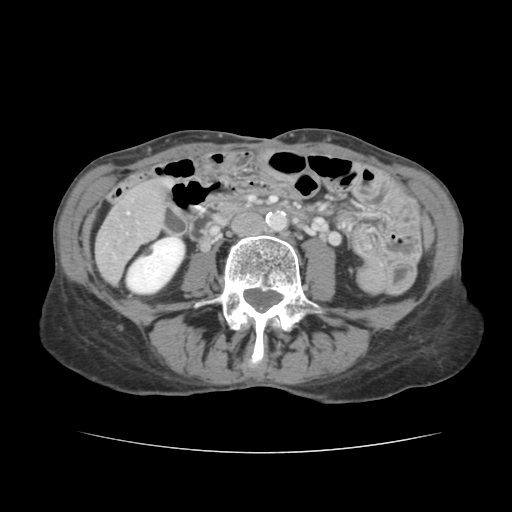
Contrast-enhanced abdominal CT, one axial slice; position 27 of 136 along the scan axis; 120 kVp; intravenous contrast given; soft-tissue window (W 400 / L 40 HU); 2.5 mm slice thickness; 512 × 512 image matrix, field of view 319 × 319 mm. Female patient, age 77 years. From the clinical record (not read from this slice): diagnosis: colorectal cancer liver metastases, imaged before liver resection; multiple liver metastases: yes; largest metastasis: 3 cm; disease in both lobes: no.
Annotated regions visible in this slice (expert manual segmentation):
- liver: bounding box <97,180,166,281> (left, top, right, bottom; pixels)